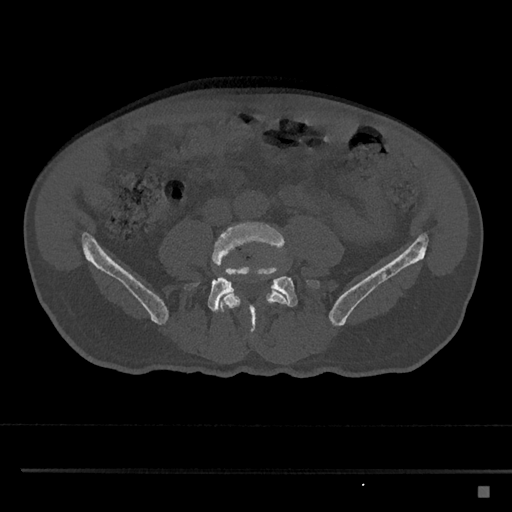
CT including the spine, one axial slice. Slice 606 of 797 in the series (ordered by position). 120 kVp. Bone window (W 1800 / L 400 HU). 0.5 mm slice thickness. 512 × 512 image matrix. Patient: male, 59 years. From the clinical record (not read from this slice): primary cancer: prostate.
Structures marked on this image (semi-automatic segmentation, software-assisted and operator-edited):
- L4 vertebra: bounding box <212,222,289,327> (left, top, right, bottom; pixels)
- L5 vertebra: <183,262,321,337>